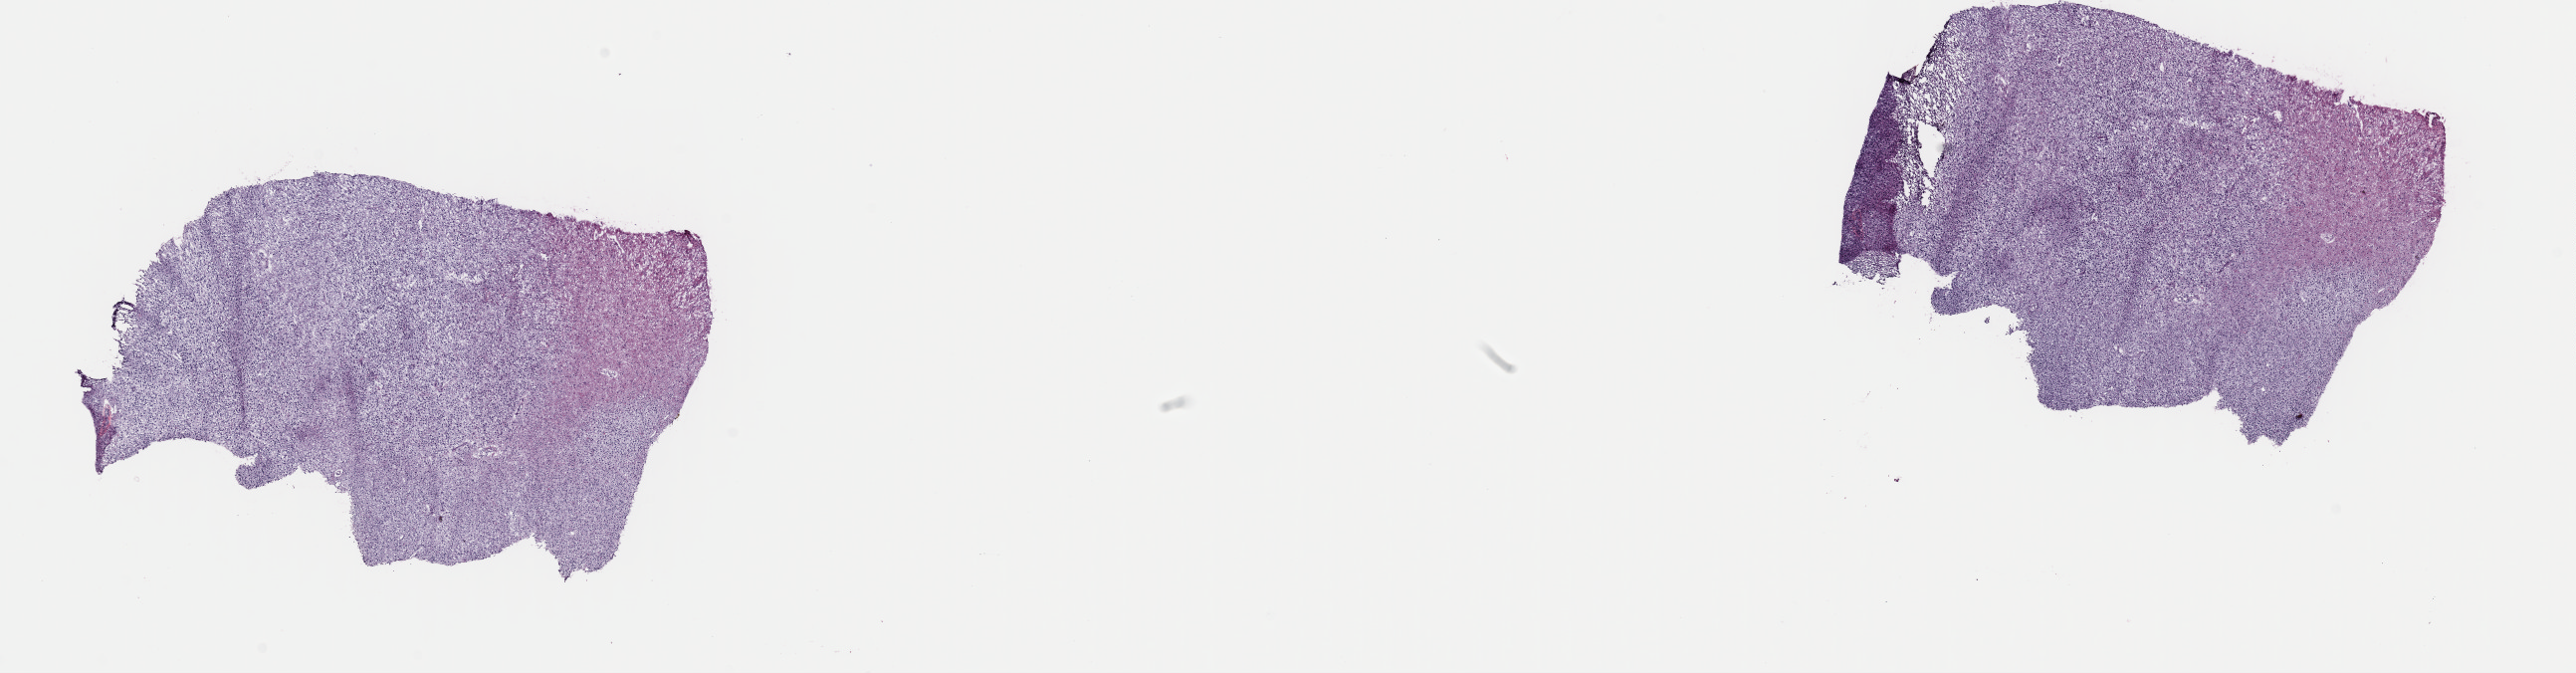
Digitized H&E-stained tissue section (whole slide) — whole scanned area (about 20.4 x 5.3 mm) shown as a low-resolution overview, frozen section from the top of the tissue portion, brain, primary tumour sample. Male, age 60 years at initial diagnosis. Histologic grade: G2 (moderately differentiated). Pathologist review of this section (percent, as recorded): tumour cells 85%, tumour nuclei 90%, normal cells 5%, stromal cells 10%, necrosis 0%. Infiltration values recorded for this section: lymphocyte infiltration 0%, monocyte infiltration 0%, neutrophil infiltration 0%.
Diagnosis: Oligodendroglioma, NOS.